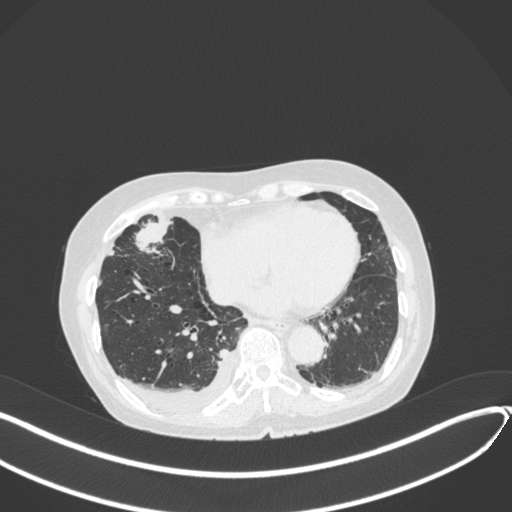
Chest CT, one axial slice; position 128 of 418 along the scan axis; reconstruction kernel B31f; lung window (W 1500 / L -600 HU); 1 mm slice thickness; 512 × 512 image matrix. Patient: female, 75 years. From the clinical record (not read from this slice): clinical TNM (as recorded): T2a N3 M0.
Structures marked on this image (rectangle marked by the reading radiologist):
- lung tumour (recorded histology: adenocarcinoma): box from (x=136, y=214) to (x=176, y=254) px